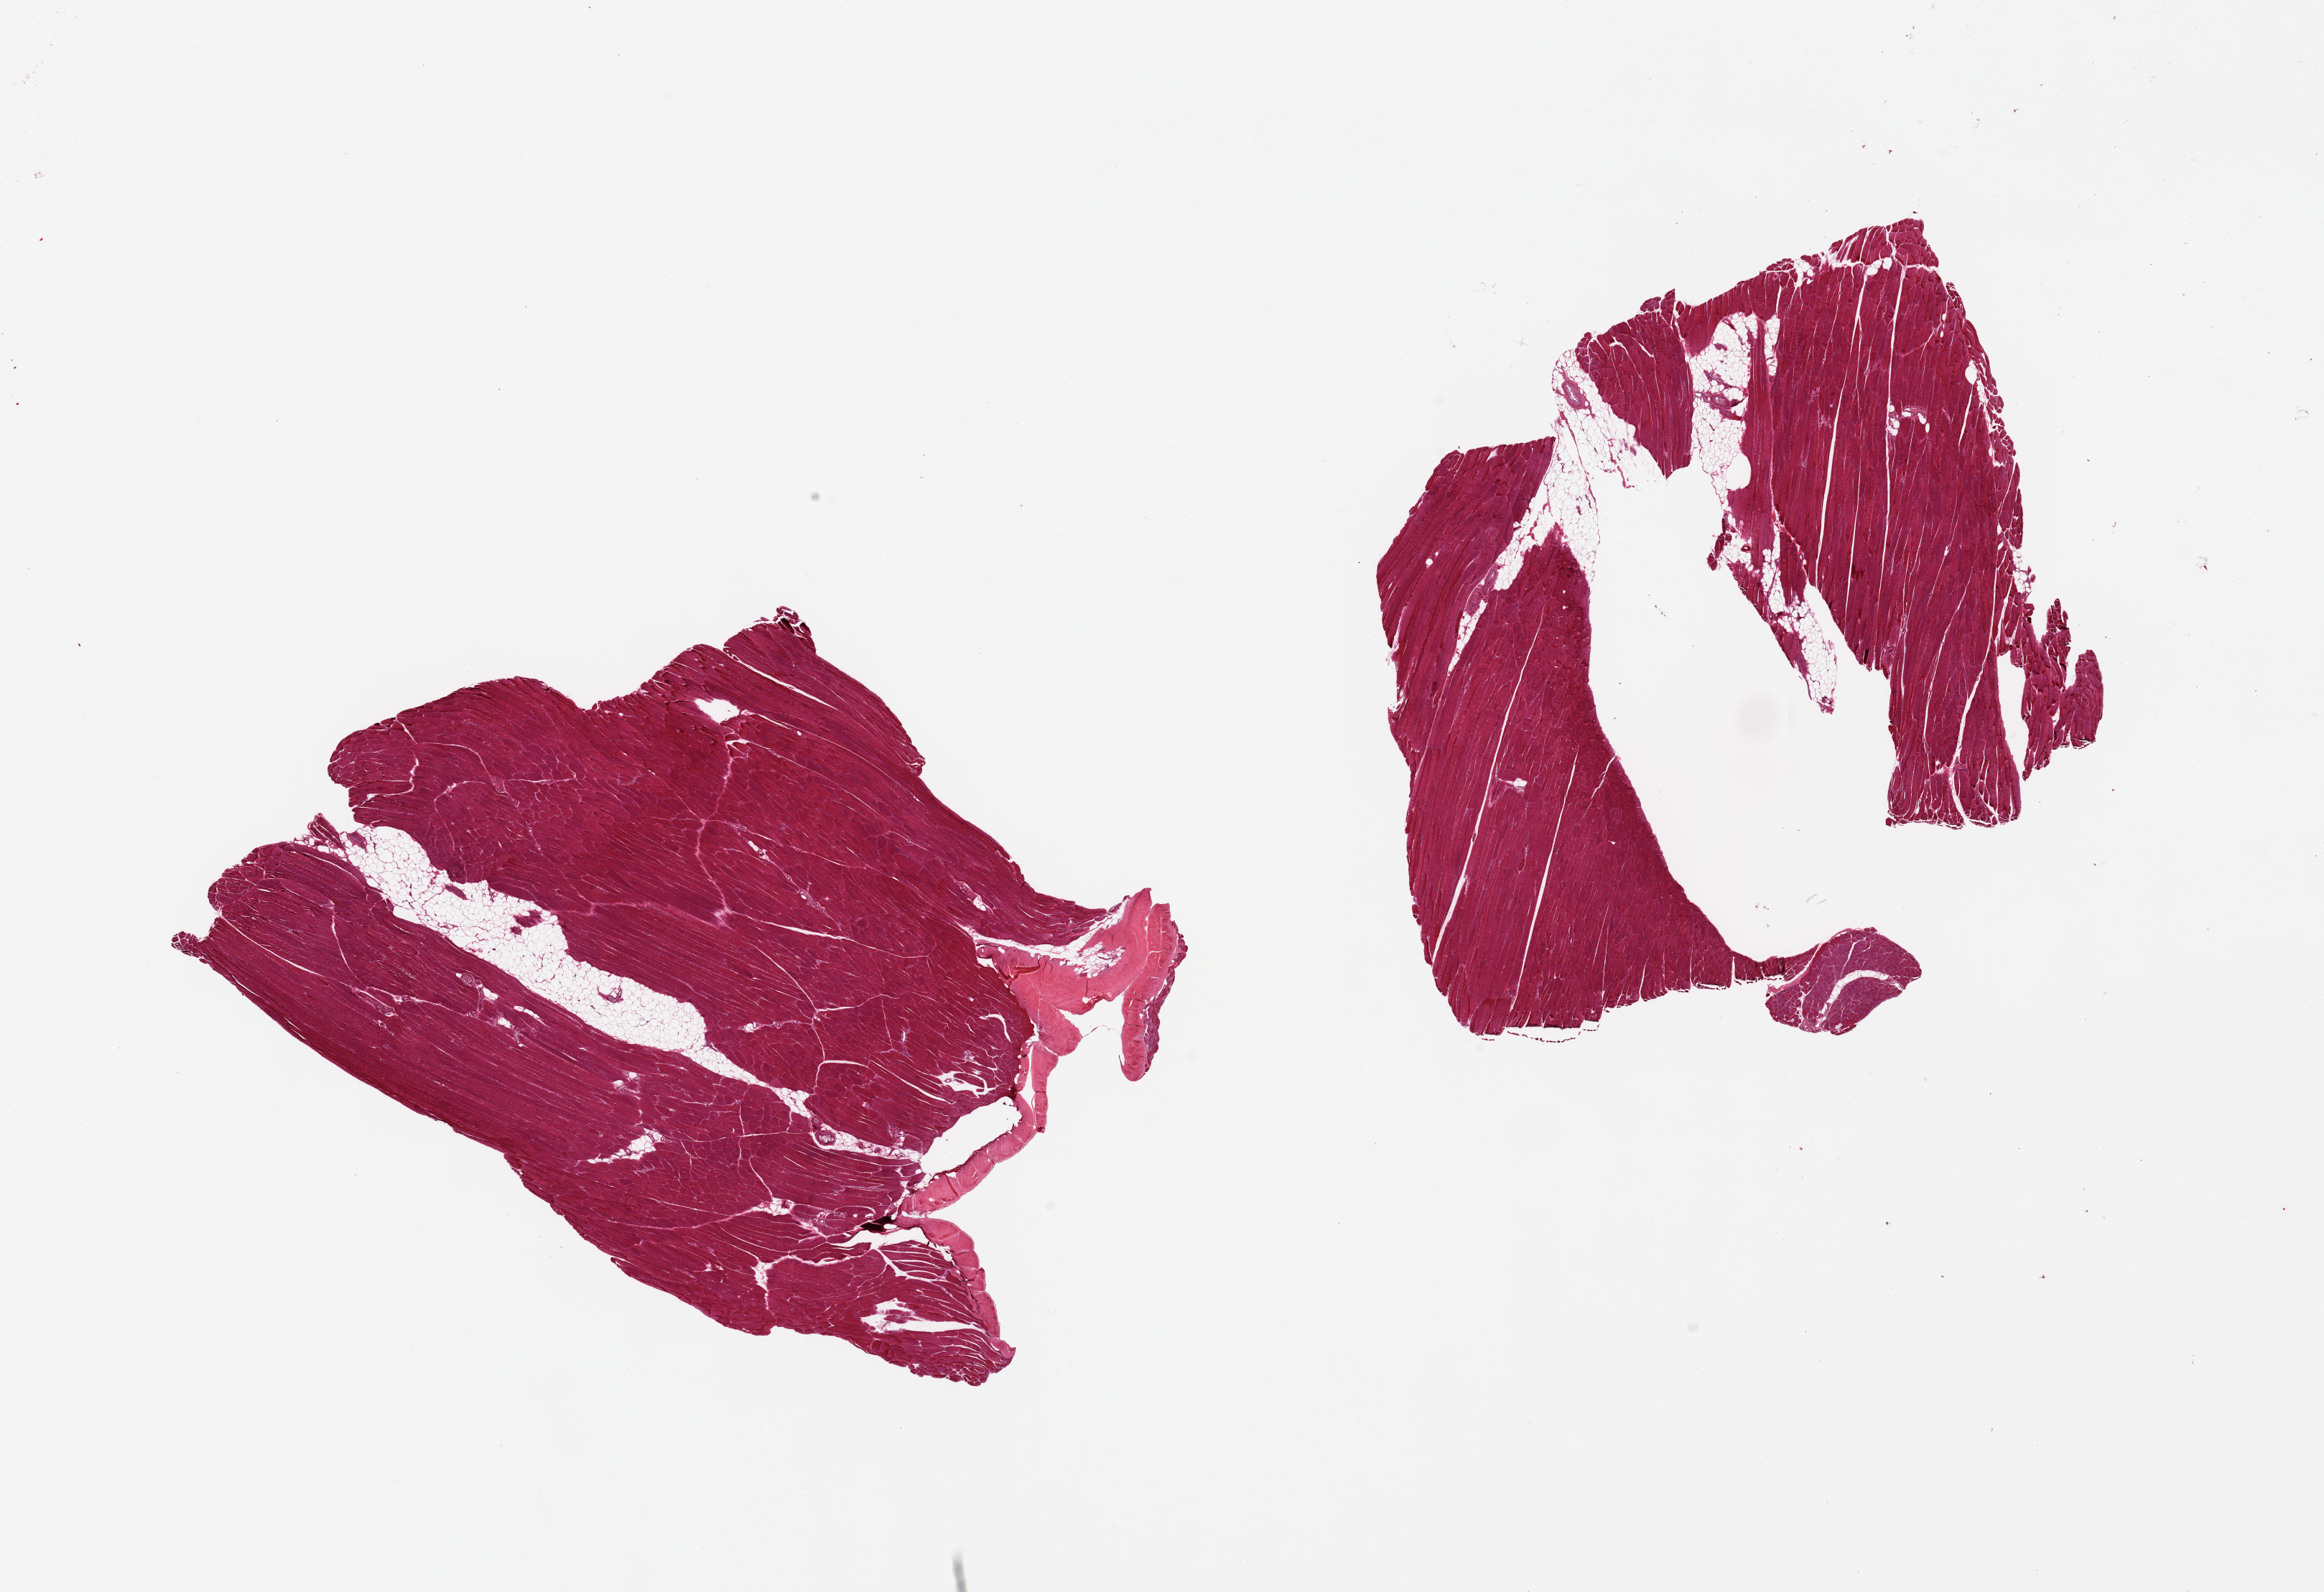
H&E whole-slide image, low-resolution overview of the scanned area, about 25.6 x 17.5 mm (slide scanned at 20x), PAXgene-fixed paraffin-embedded (PFPE) section, section of skeletal muscle (target tissue), tissue donor sample. Donor: female.
Reviewer comment on this tissue sample: 2 pieces, ~10% interstitial fat.